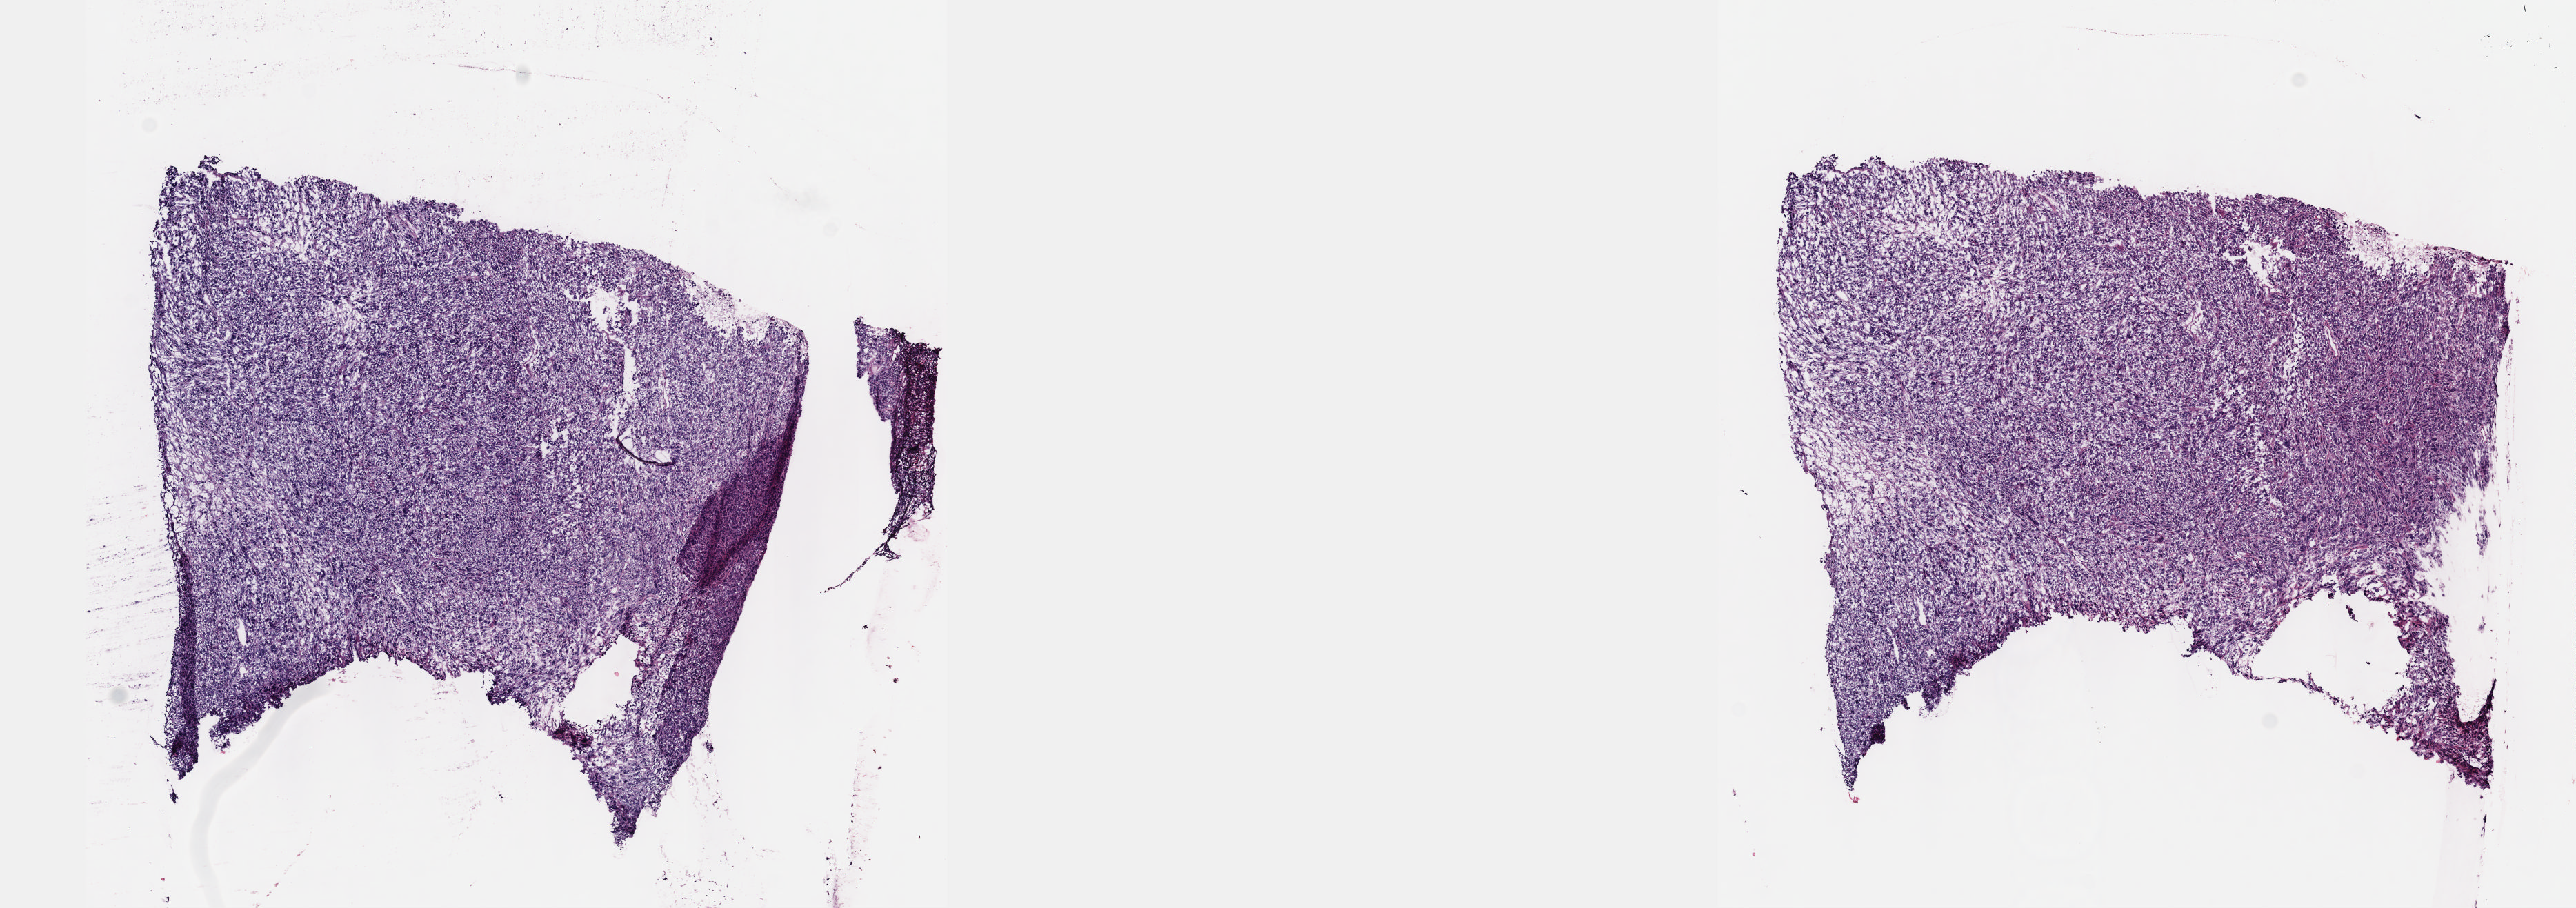
Digitized Hematoxylin and eosin (H&E) stained tissue section (whole slide), whole scanned area (about 15.1 x 5.3 mm) shown as a low-resolution overview. Frozen section from the top of the tissue portion. Sample: recurrent tumour, connective, subcutaneous and other soft tissues. Patient: female, age at initial diagnosis 49 years. Slide review estimates, as recorded: tumour cells 100%, tumour nuclei 97%, normal cells 0%, stromal cells 0%, necrosis 0%. Infiltration values recorded for this section: lymphocyte infiltration 0%, monocyte infiltration 0%, neutrophil infiltration 0%.
This section: recurrent tumour. Patient diagnosis: Undifferentiated sarcoma (connective, subcutaneous and other soft tissues of lower limb and hip).